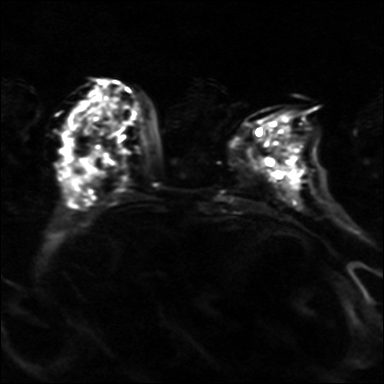
Breast MRI, one axial slice; slice 14 of 36 in the series (ordered by position); diffusion-weighted series; image 2 of 4 stored at this slice position (different b-values; order by instance number); 3 T; 4 mm slice thickness; 384 × 384 image matrix. Female patient.
Outlined on this slice (expert manual segmentation):
- tumour on diffusion-weighted imaging: bounding box [x1, y1, x2, y2] px = [285, 148, 299, 188]